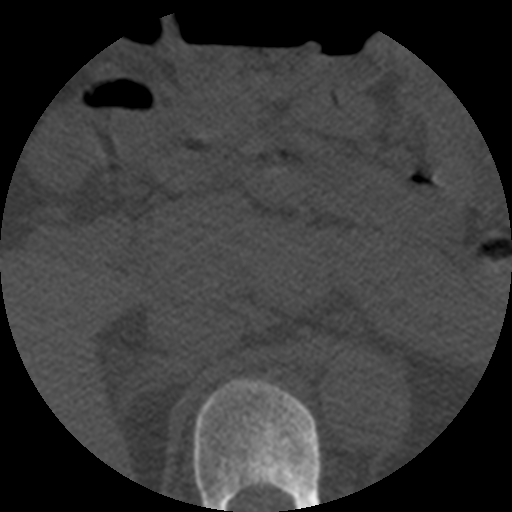
CT including the spine, one axial slice. Position 239 of 508 along the scan axis. 120 kVp. Bone window (W 1800 / L 400 HU). 512 × 512 image matrix, field of view 160 × 160 mm. Patient age 57 years. Case-level facts recorded for this patient, not image findings: primary cancer: prostate.
Annotated regions visible in this slice (semi-automatically segmented with operator editing):
- T11 vertebra: bounding box (x1, y1, x2, y2) in pixels: (193, 379, 322, 512)